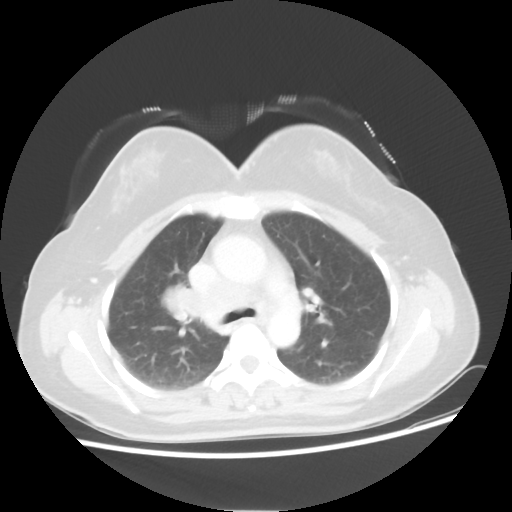
Chest CT, one axial slice. Slice 34 of 50 in the series (ordered by position). Reconstruction kernel STANDARD. Lung window (W 1500 / L -600 HU). 512 × 512 image matrix. Female patient, age 40 years. Case-level facts recorded for this patient, not image findings: clinical TNM (as recorded): T1c N3 M0.
Outlined on this slice (bounding box drawn by a radiologist):
- lung tumour (recorded histology: small cell carcinoma): bounding box <163,283,198,324> (left, top, right, bottom; pixels)